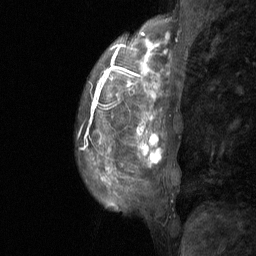
Breast MRI (dynamic contrast-enhanced), one sagittal slice; position 20 of 64 along the scan axis; dynamic contrast-enhanced study with each time point stored as its own series, time point 2 of 3 at this slice position (early post-contrast, ordered by acquisition time); 1.5 T; TE 4.8 ms, TR 27 ms; 2 mm slice thickness; 256 × 256 image matrix. Patient: female, 36 years. From the clinical record (not read from this slice): setting: breast cancer imaged before/during neoadjuvant chemotherapy; receptor status: HR-positive, HER2-negative.
Annotated regions visible in this slice (semi-automatically segmented with operator editing):
- analysis volume of interest (the breast-tissue region the enhancement analysis was run in; not a lesion): bounding box <76,12,198,232> (left, top, right, bottom; pixels)
- tumour enhancement mask (voxels above the 90 % enhancement threshold inside the analysis volume of interest): <141,33,169,167>